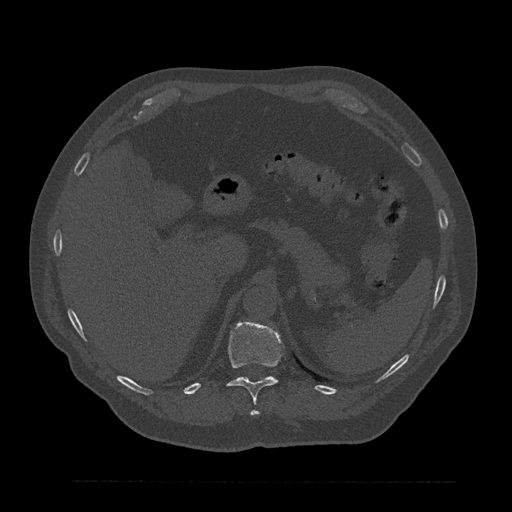
CT including the spine, one axial slice. Slice 284 of 797 in the series (ordered by position). Reconstruction kernel Br40s/3. Bone window (W 1800 / L 400 HU). 0.5 mm slice thickness. 512 × 512 image matrix, field of view 430 × 430 mm. Patient: male, 61 years. Case-level facts recorded for this patient, not image findings: primary cancer: prostate.
Outlined on this slice (semi-automatically segmented with operator editing):
- T11 vertebra: box from (x=227, y=321) to (x=281, y=415) px